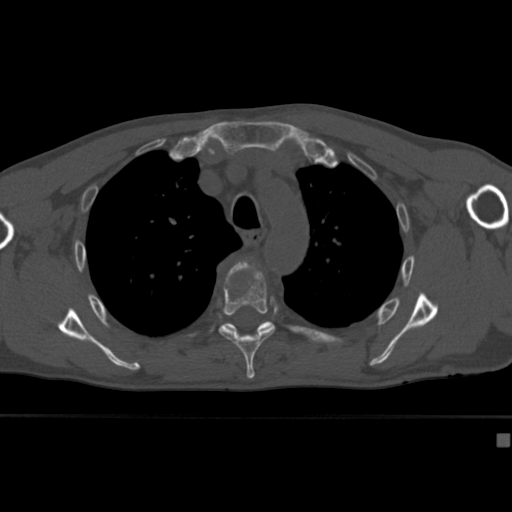
CT including the spine, one axial slice; position 308 of 430 along the scan axis; reconstruction kernel Br40s; 120 kVp; bone window (W 1800 / L 400 HU); 1.5 mm slice thickness; 512 × 512 image matrix, field of view 337 × 337 mm. Patient: male, 64 years. Case-level facts recorded for this patient, not image findings: primary cancer: uterus; vertebrae with lytic lesions (as recorded): T1, T4, T5, T7, L5.
Structures marked on this image (semi-automatically segmented with operator editing):
- T4 vertebra: bounding box [x1, y1, x2, y2] px = [227, 257, 261, 278]
- T5 vertebra: [219, 269, 276, 381]
- T6 vertebra: [223, 320, 272, 333]